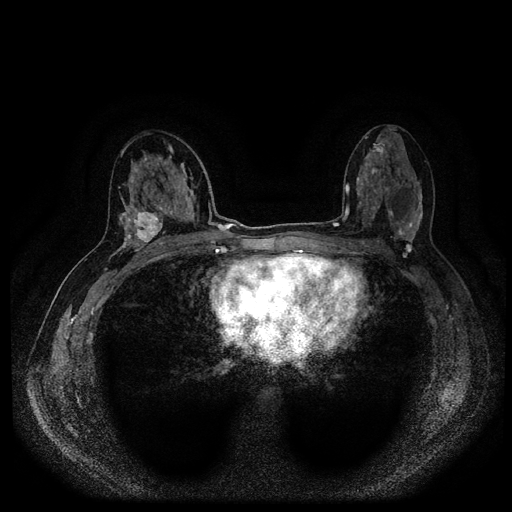
Breast MRI (dynamic contrast-enhanced, multi-phase), one axial slice; slice 54 of 116 in the series (ordered by position); dynamic contrast-enhanced series, time point 2 of 5 at this slice position (early post-contrast); 1.5 T; TE 2.6 ms, TR 5.4 ms; 512 × 512 image matrix, field of view 340 × 340 mm. Female patient, age 48 years.
Structures marked on this image (semi-automatically segmented with operator editing):
- breast lesion (labelled 'tumour' in the annotation; benign lesions carry a separate 'benign' label): box from (x=132, y=208) to (x=163, y=248) px